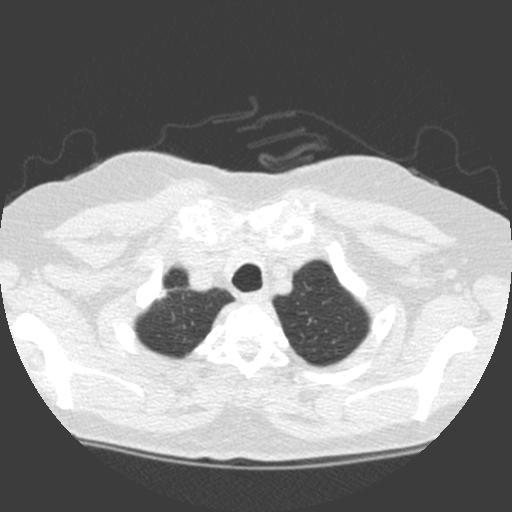
Low-dose screening chest CT, one axial slice; slice 144 of 155 in the series (ordered by position); lung window (W 1500 / L -600 HU); 512 × 512 image matrix, field of view 314 × 314 mm.
Outlined on this slice (outlined manually by an expert reader):
- lesion 1 (tumor, upper lobe of right lung): bounding box (x1, y1, x2, y2) in pixels: (157, 289, 169, 301)